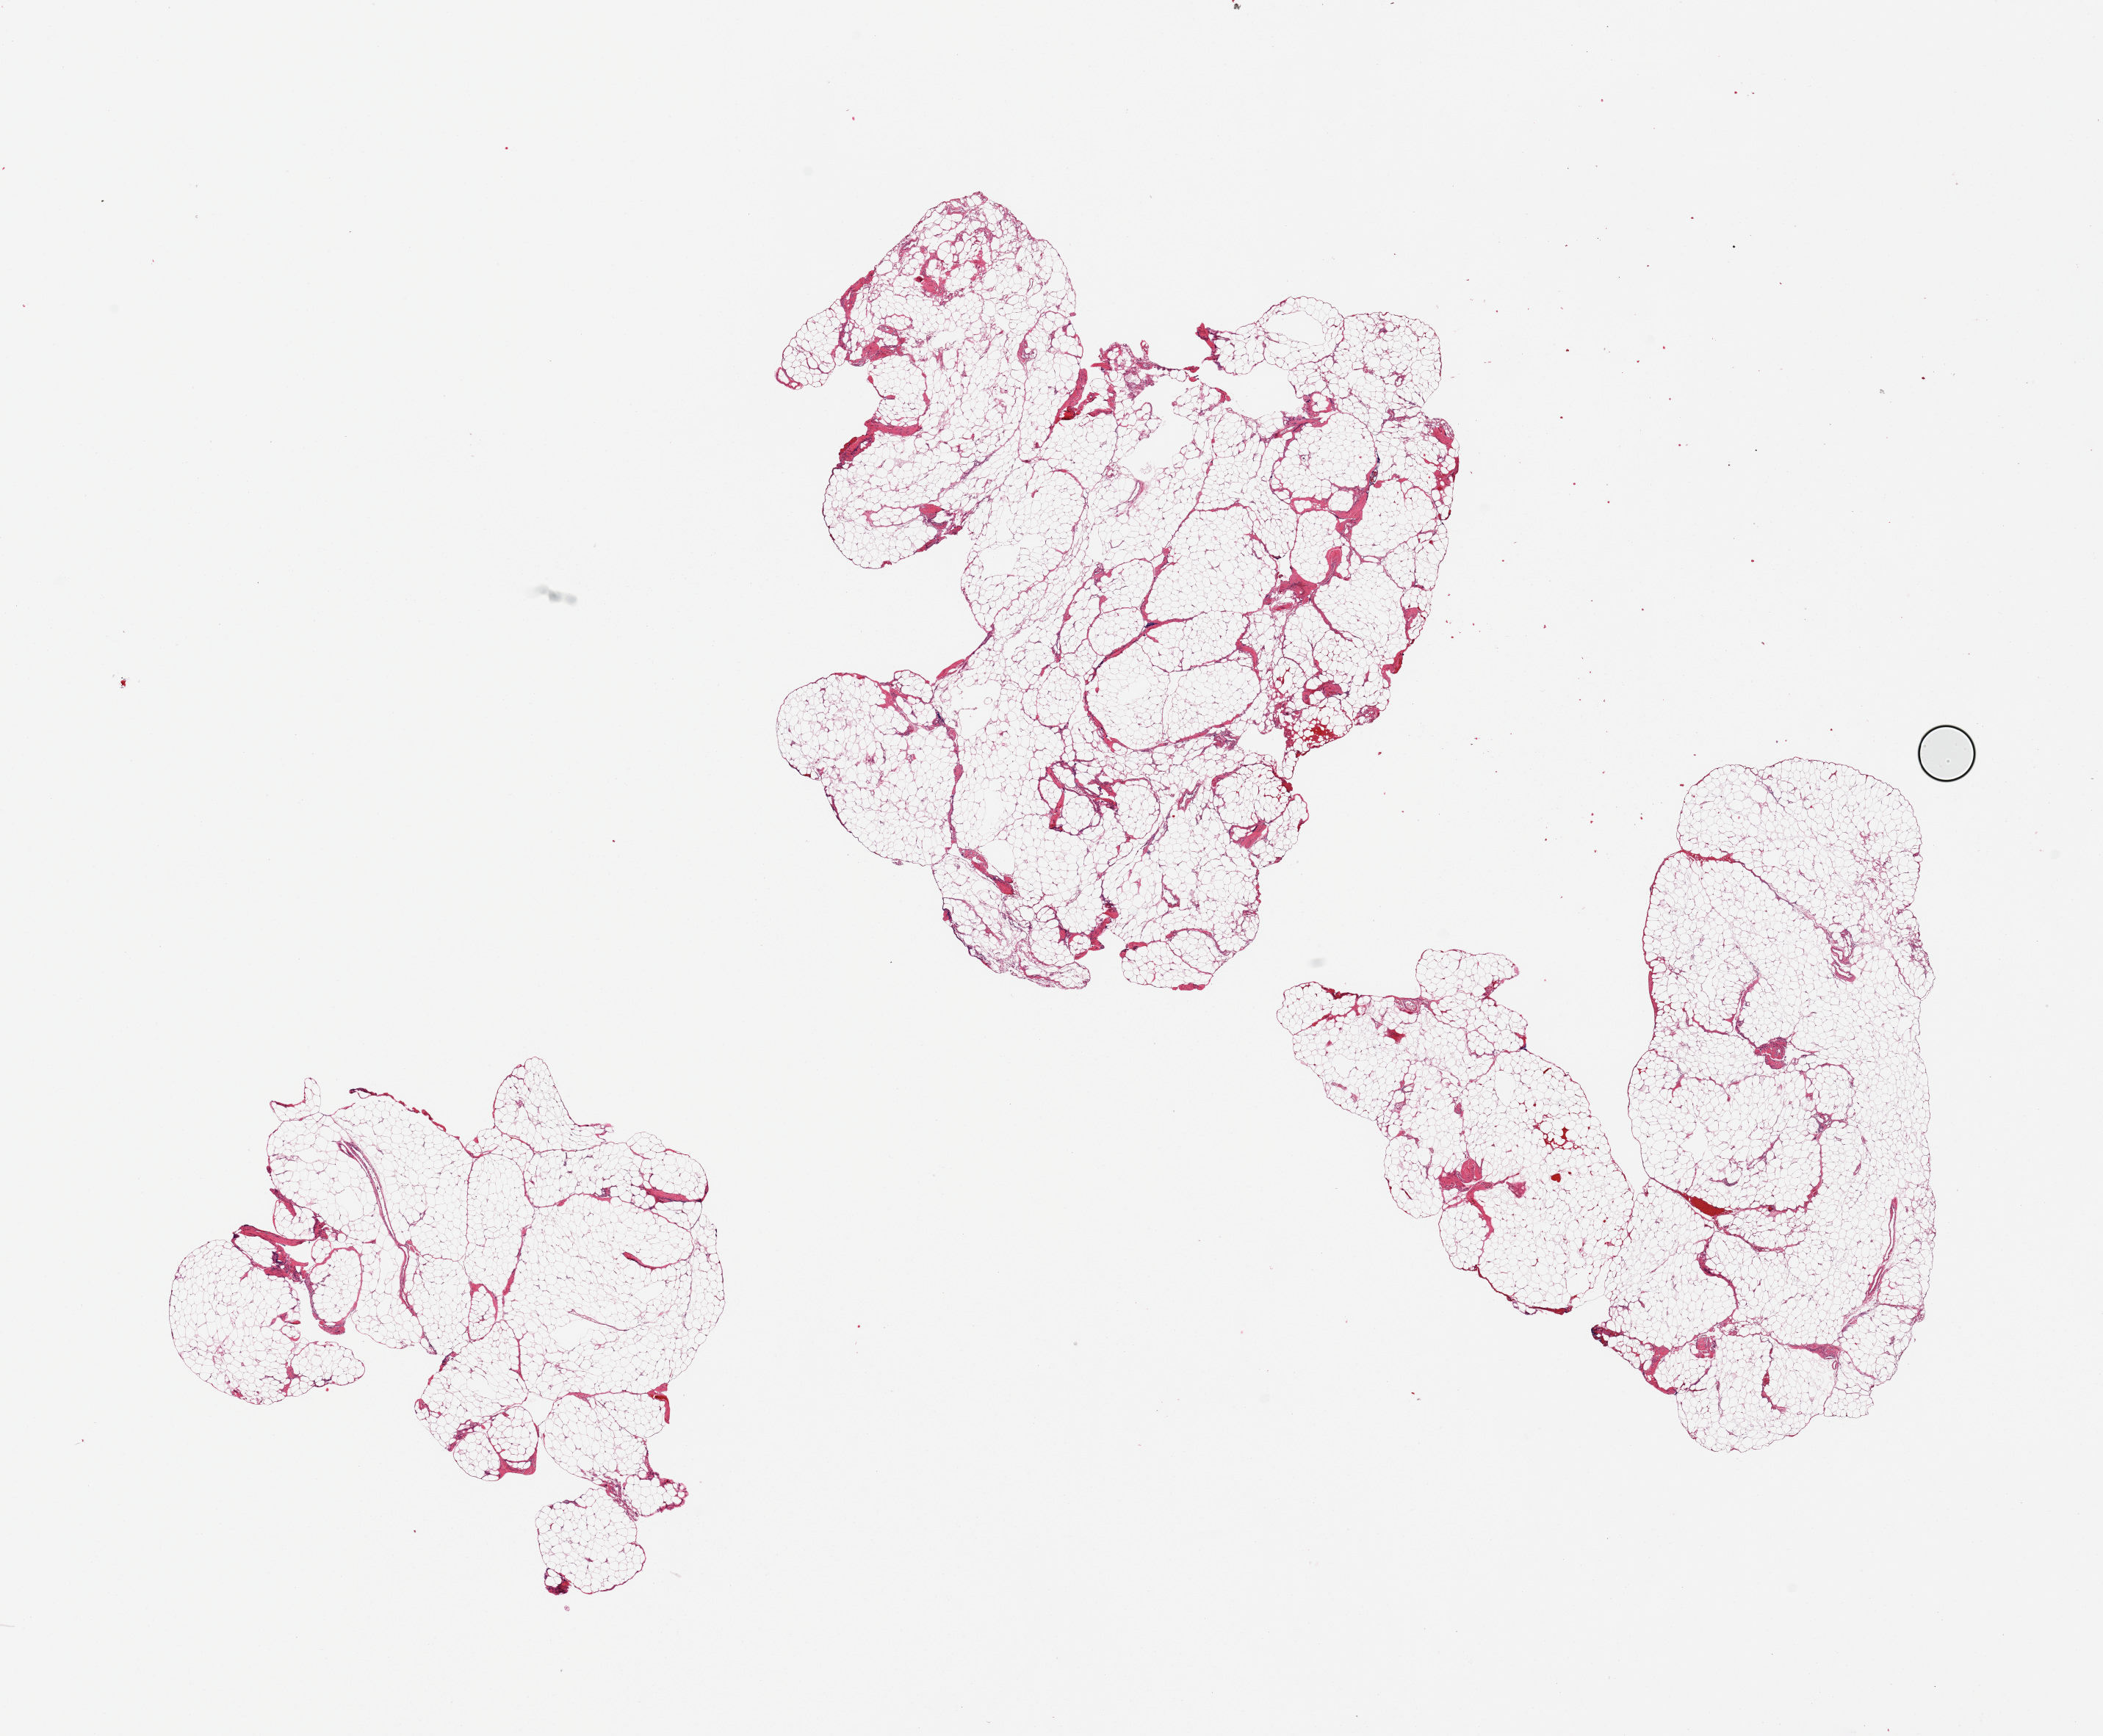
Hematoxylin and eosin (H&E) whole-slide image, low-resolution overview of the scanned area, about 22.6 x 18.7 mm (from a 20x scan); PAXgene-fixed paraffin-embedded (PFPE) section; sampled site (target tissue): omentum; tissue donor sample. Donor: male.
Pathologist's review note for this sample: 2 pieces.